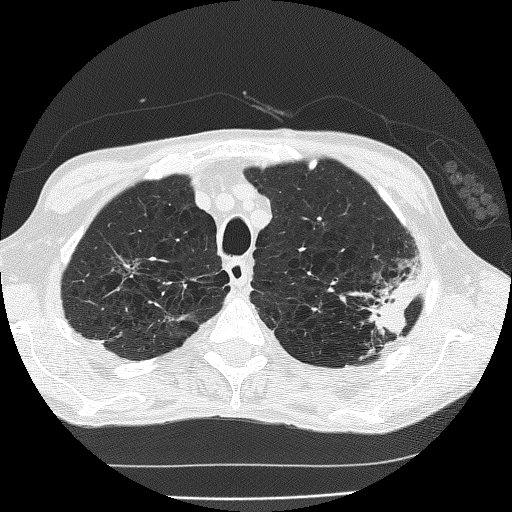
Low-dose screening chest CT, one axial slice; slice 151 of 185 in the series (ordered by position); 120 kVp; lung window (W 1500 / L -600 HU); 2 mm slice thickness; 512 × 512 image matrix.
Outlined on this slice (manually delineated by an expert):
- lesion 1 (tumor, upper lobe of left lung): box from (x=368, y=276) to (x=421, y=335) px